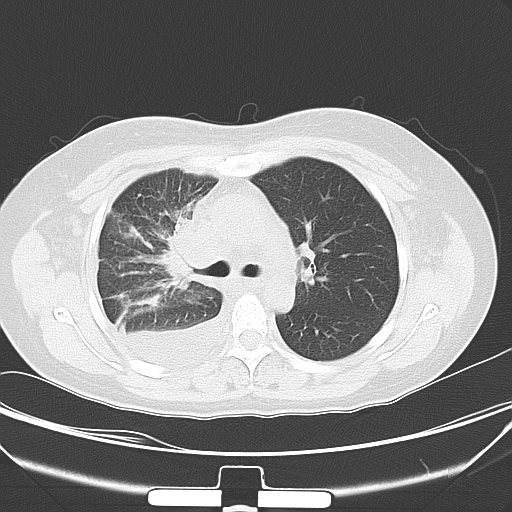
Chest CT, one axial slice. Slice 35 of 52 in the series (ordered by position). 120 kVp. Lung window (W 1500 / L -600 HU). 512 × 512 image matrix, field of view 352 × 352 mm. Patient: female, 36 years. Case-level facts recorded for this patient, not image findings: clinical TNM (as recorded): T1b N2 M0; histopathological grade: G3.
Structures marked on this image (bounding box drawn by a radiologist):
- lung tumour (recorded histology: adenocarcinoma): bounding box (x1, y1, x2, y2) in pixels: (153, 204, 217, 291)